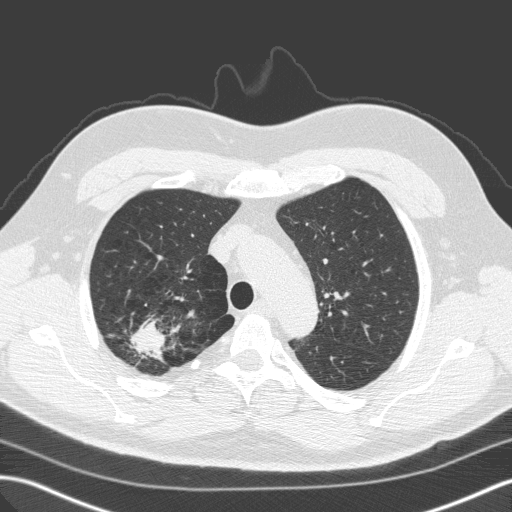
Low-dose screening chest CT, one axial slice; slice 118 of 149 in the series (ordered by position); lung window (W 1500 / L -600 HU); 512 × 512 image matrix.
Structures marked on this image (outlined manually by an expert reader):
- lesion 1 (tumor, upper lobe of right lung): bounding box (x1, y1, x2, y2) in pixels: (133, 322, 164, 354)